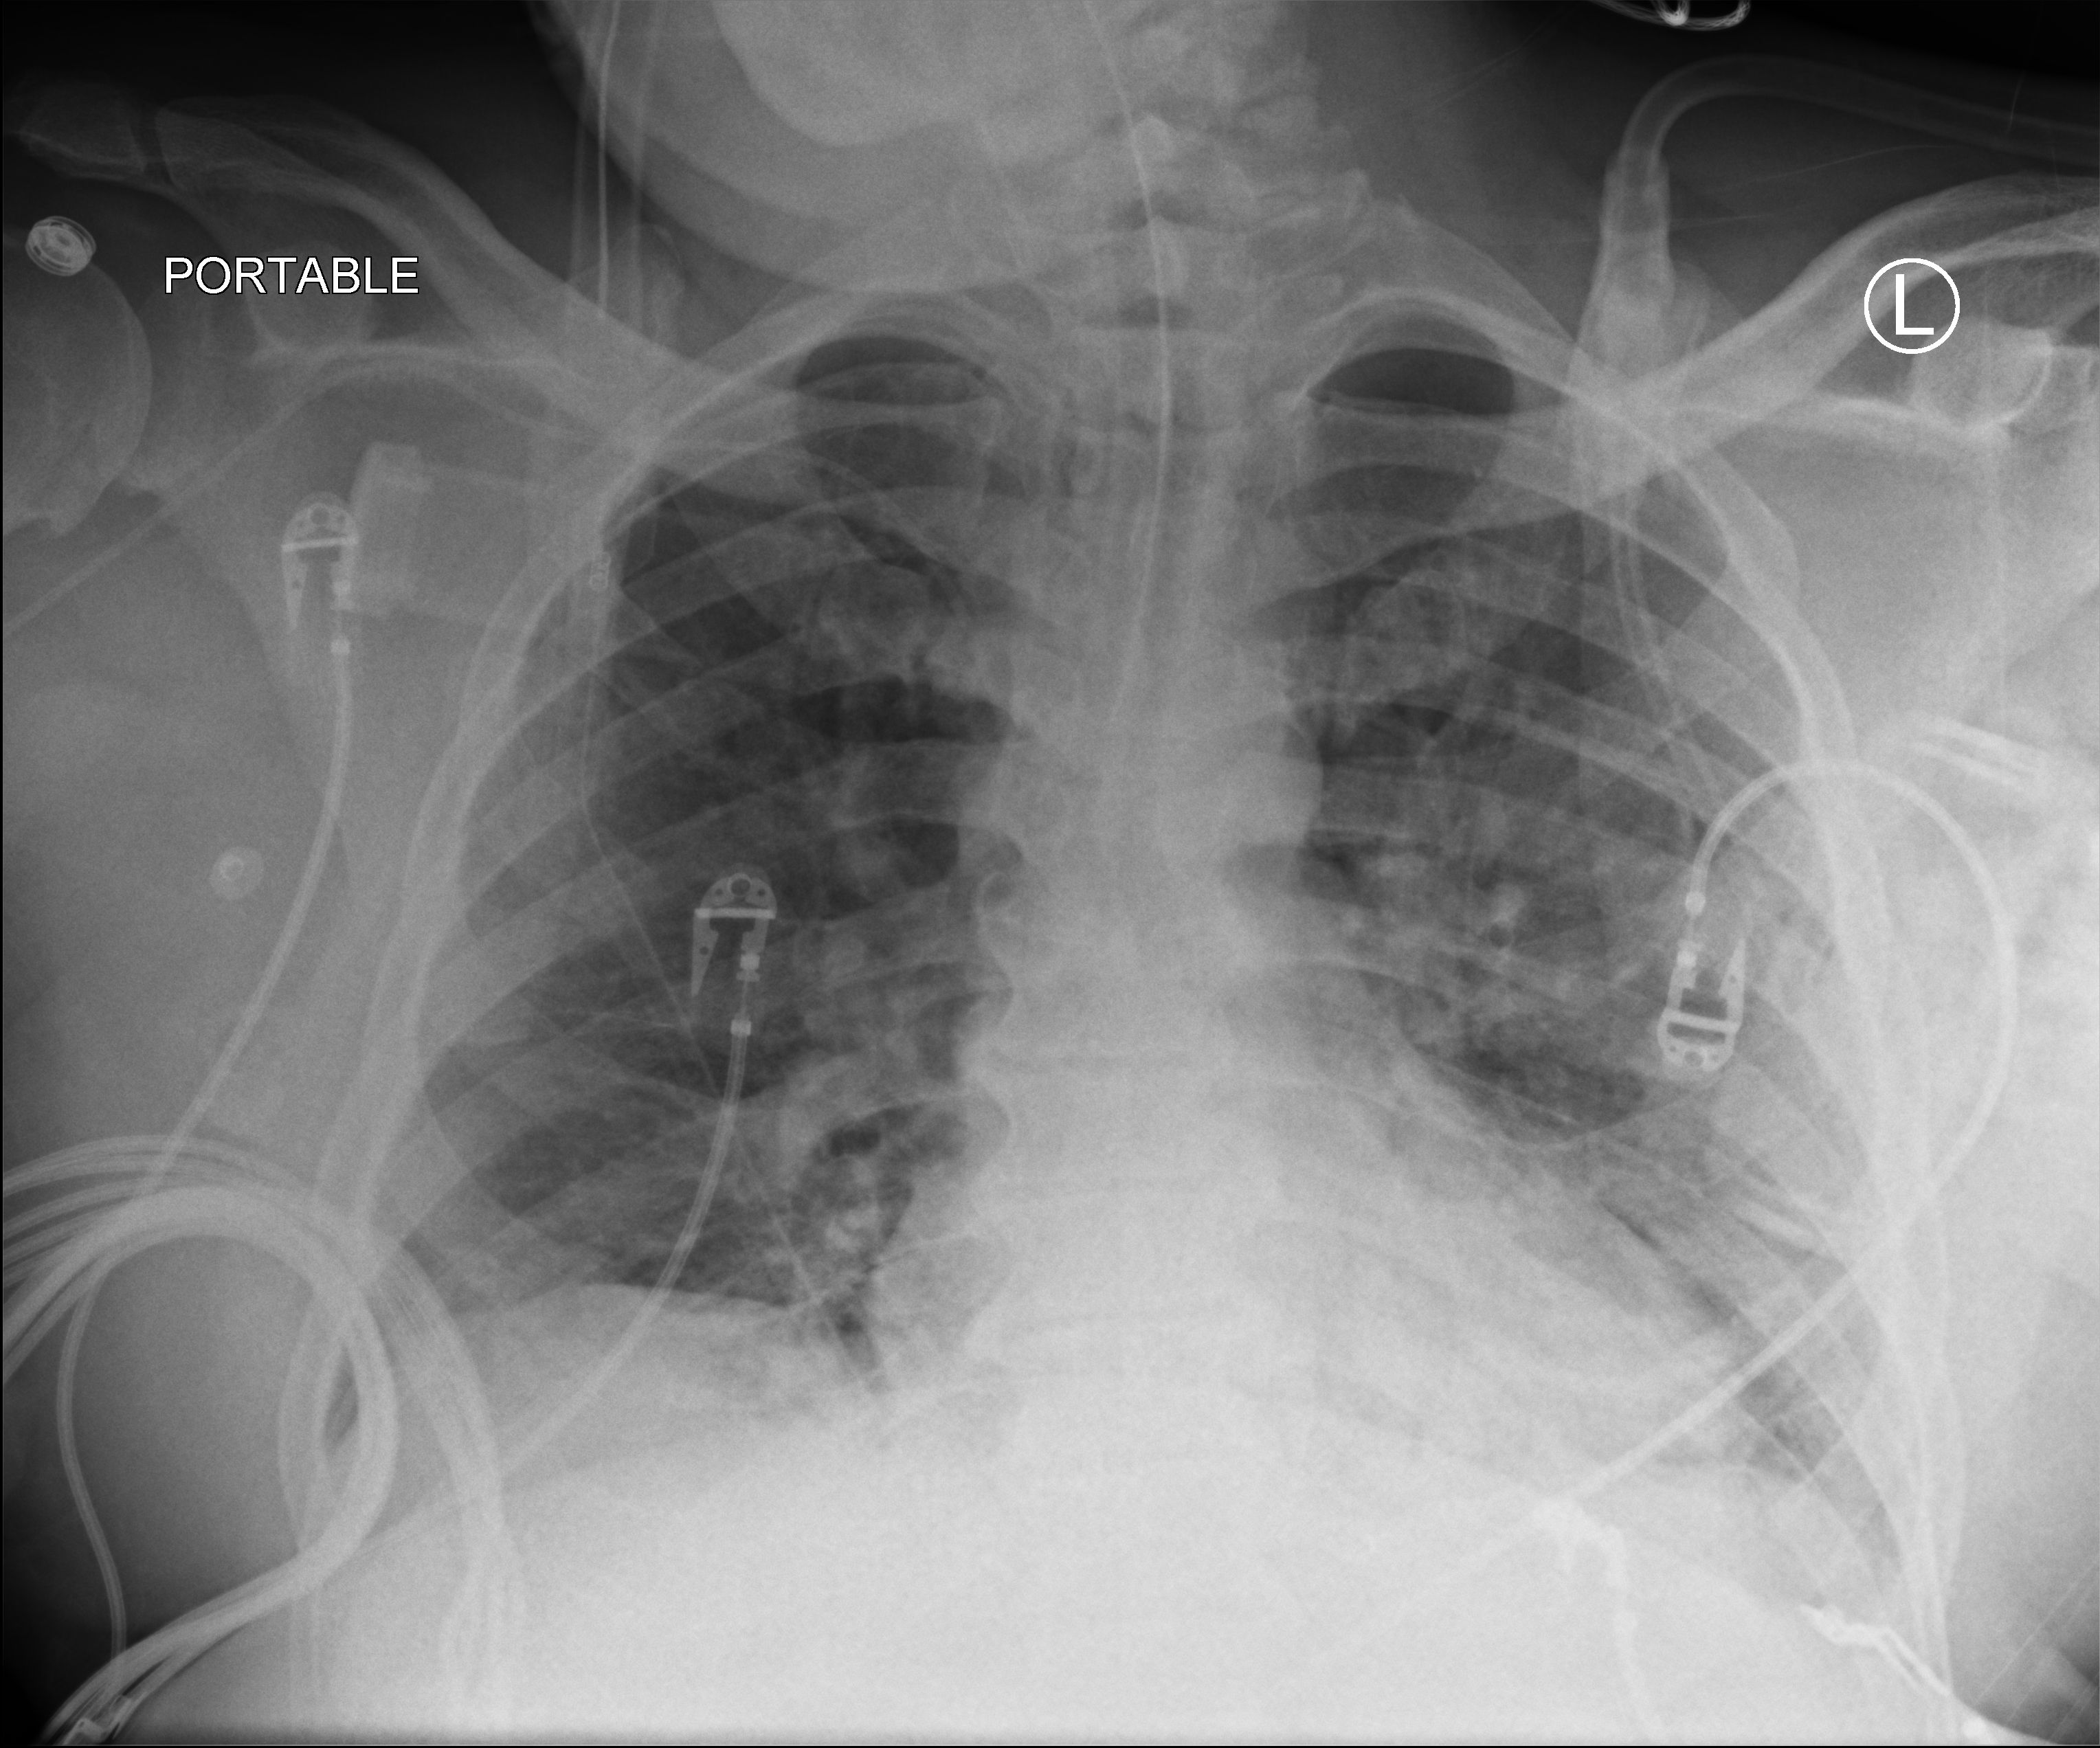
Bedside chest radiograph (computed radiography), anteroposterior (AP) projection. Patient hospitalised with COVID-19; male, aged 18–59 years.
Admission-level facts for this patient (not findings on this image; timing relative to this image not recorded):
- mechanically ventilated during this hospital stay: yes